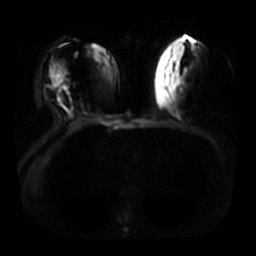
Breast MRI, one axial slice; position 14 of 31 along the scan axis; diffusion-weighted series; image 2 of 4 stored at this slice position (different b-values; order by instance number); 3 T; 256 × 256 image matrix. Female patient.
Annotated regions visible in this slice (outlined manually by an expert reader):
- tumour on diffusion-weighted imaging: bounding box <52,76,64,89> (left, top, right, bottom; pixels)